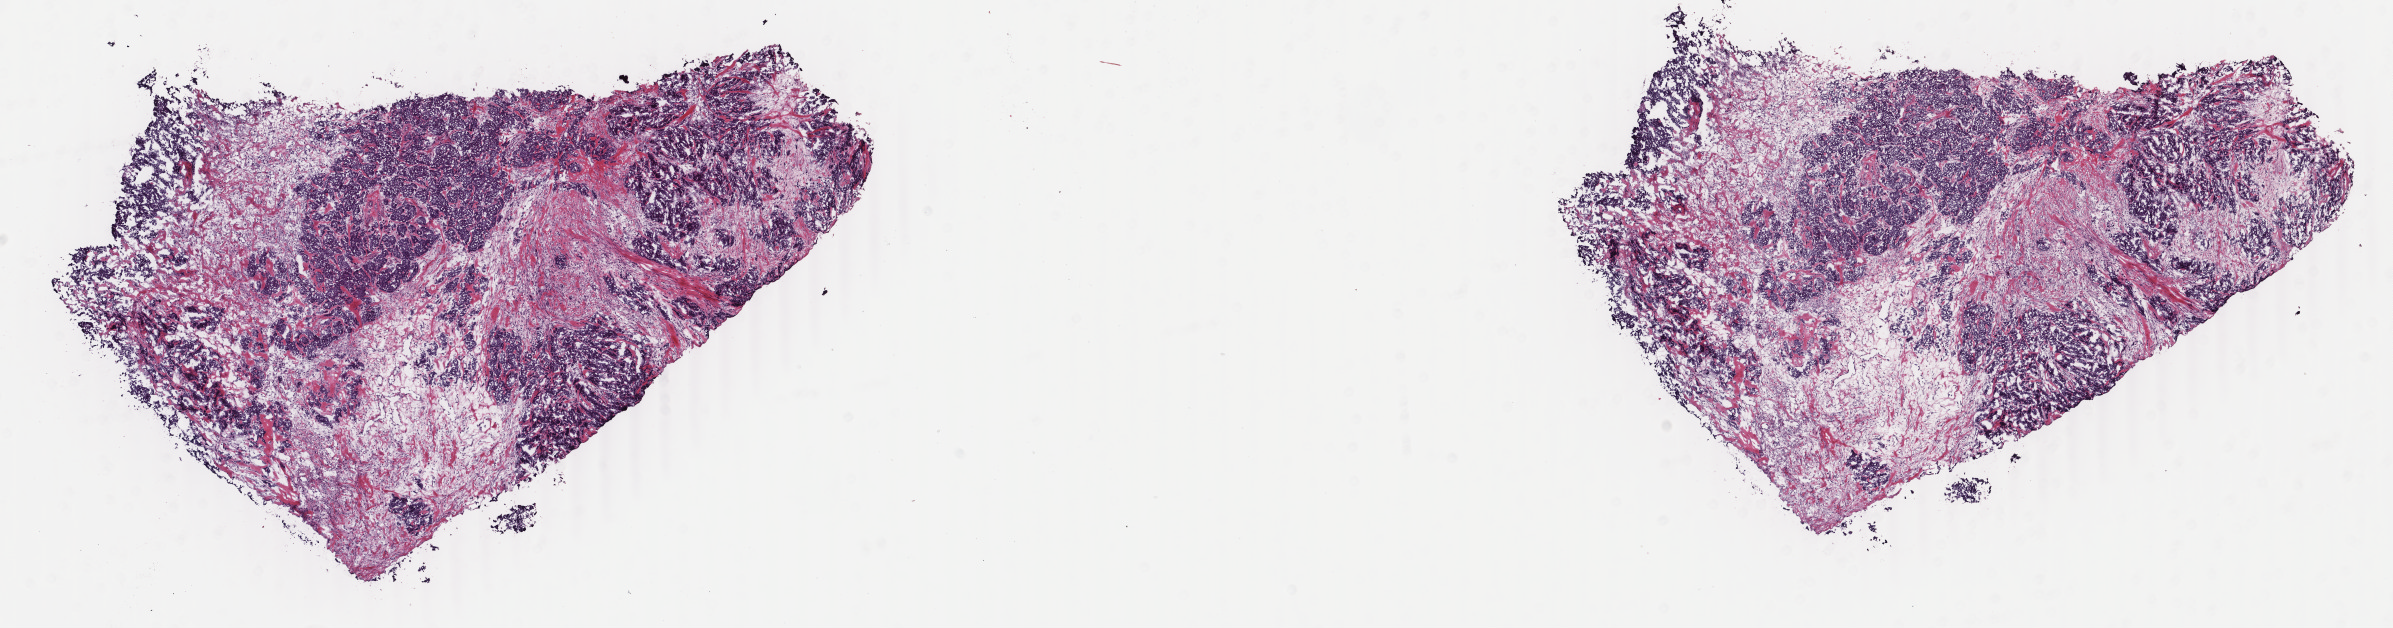
Whole-slide histology image, H&E-stained — whole scanned area (about 19.0 x 5.0 mm) shown as a low-resolution overview, frozen section from the top of the tissue portion, sample: primary tumour, breast. Patient: female, age at initial diagnosis 52 years. Pathologist review of this section (percent, as recorded): tumour cells 50%, tumour nuclei 80%, normal cells 0%, stromal cells 45%, necrosis 5%. Inflammatory infiltration, as recorded: lymphocyte infiltration 1%, monocyte infiltration 0%, neutrophil infiltration 0%.
AJCC pathologic stage: IA. Diagnosis: Infiltrating duct carcinoma, NOS. Lymph nodes positive (case pathology): 0 of 6 examined. Laterality: right.